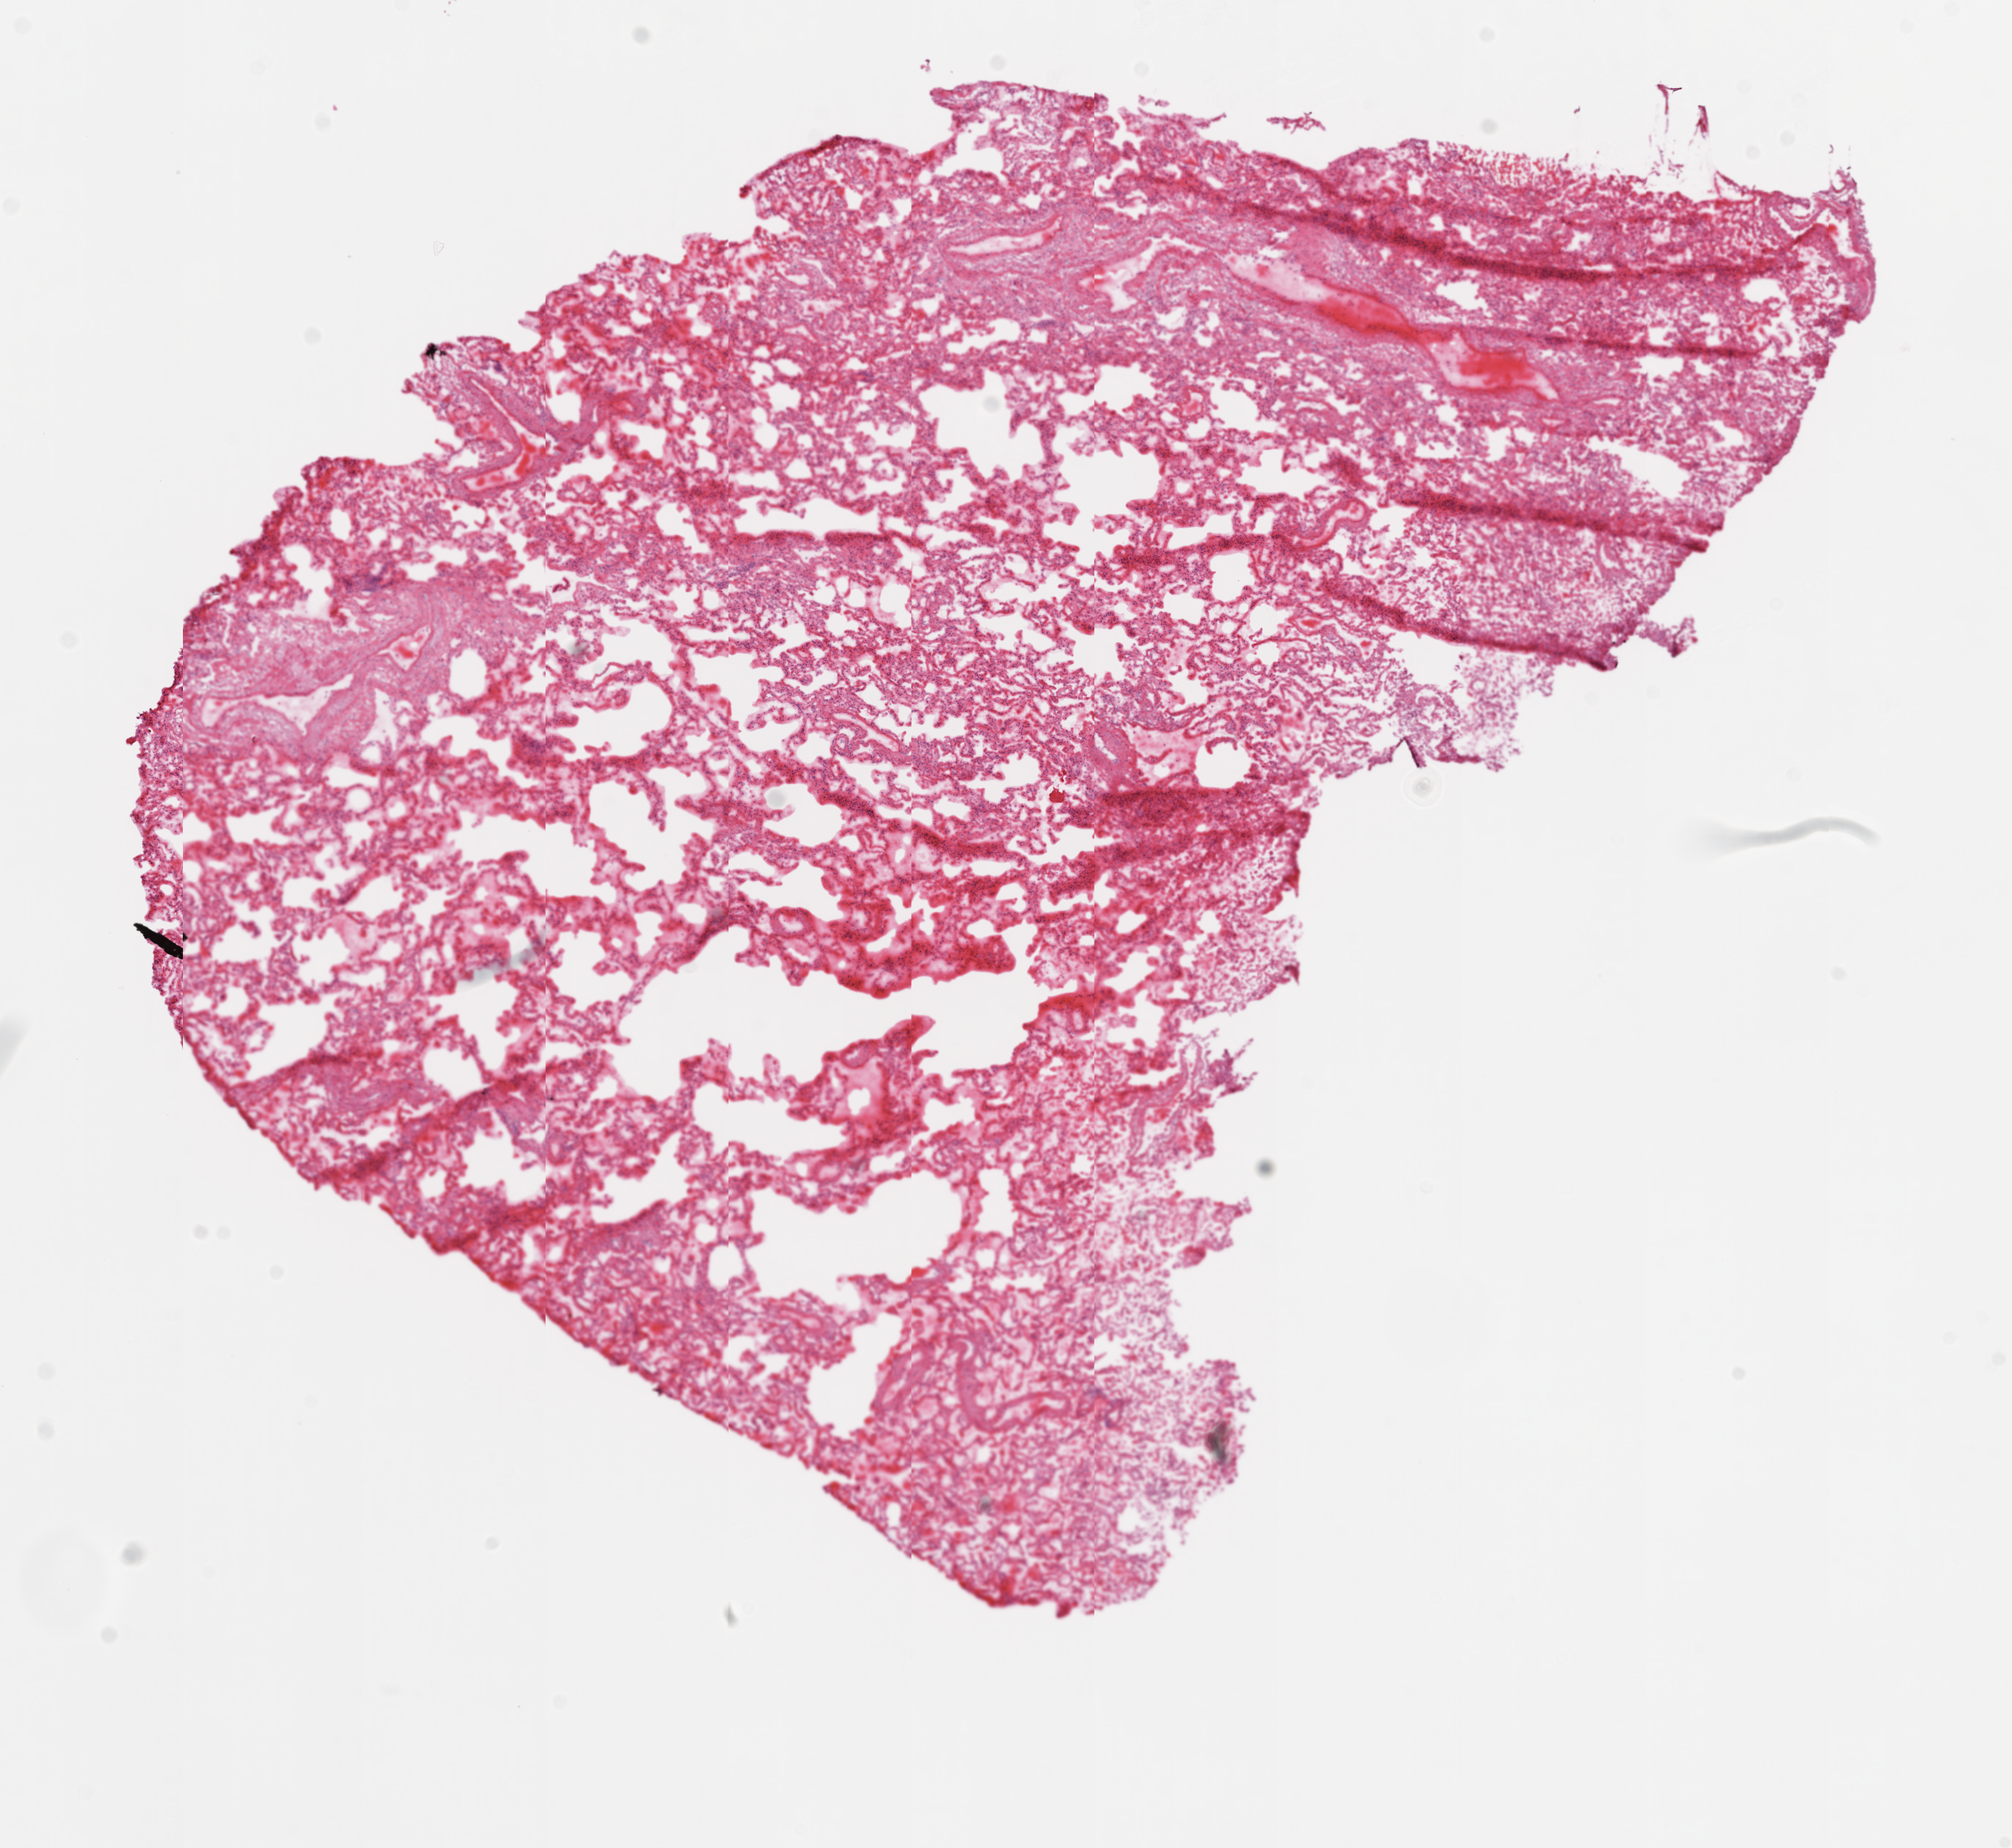
Whole-slide histology image, H&E — low-resolution overview of the scanned area, about 11.0 x 10.1 mm (acquisition: 20x scan), frozen section, sample: solid tissue normal (non-tumour tissue), lung. Male, age 78 years at initial diagnosis.
This section: solid tissue normal sample (biorepository sample class). Patient diagnosis: Squamous cell carcinoma, NOS (lower lobe, lung).